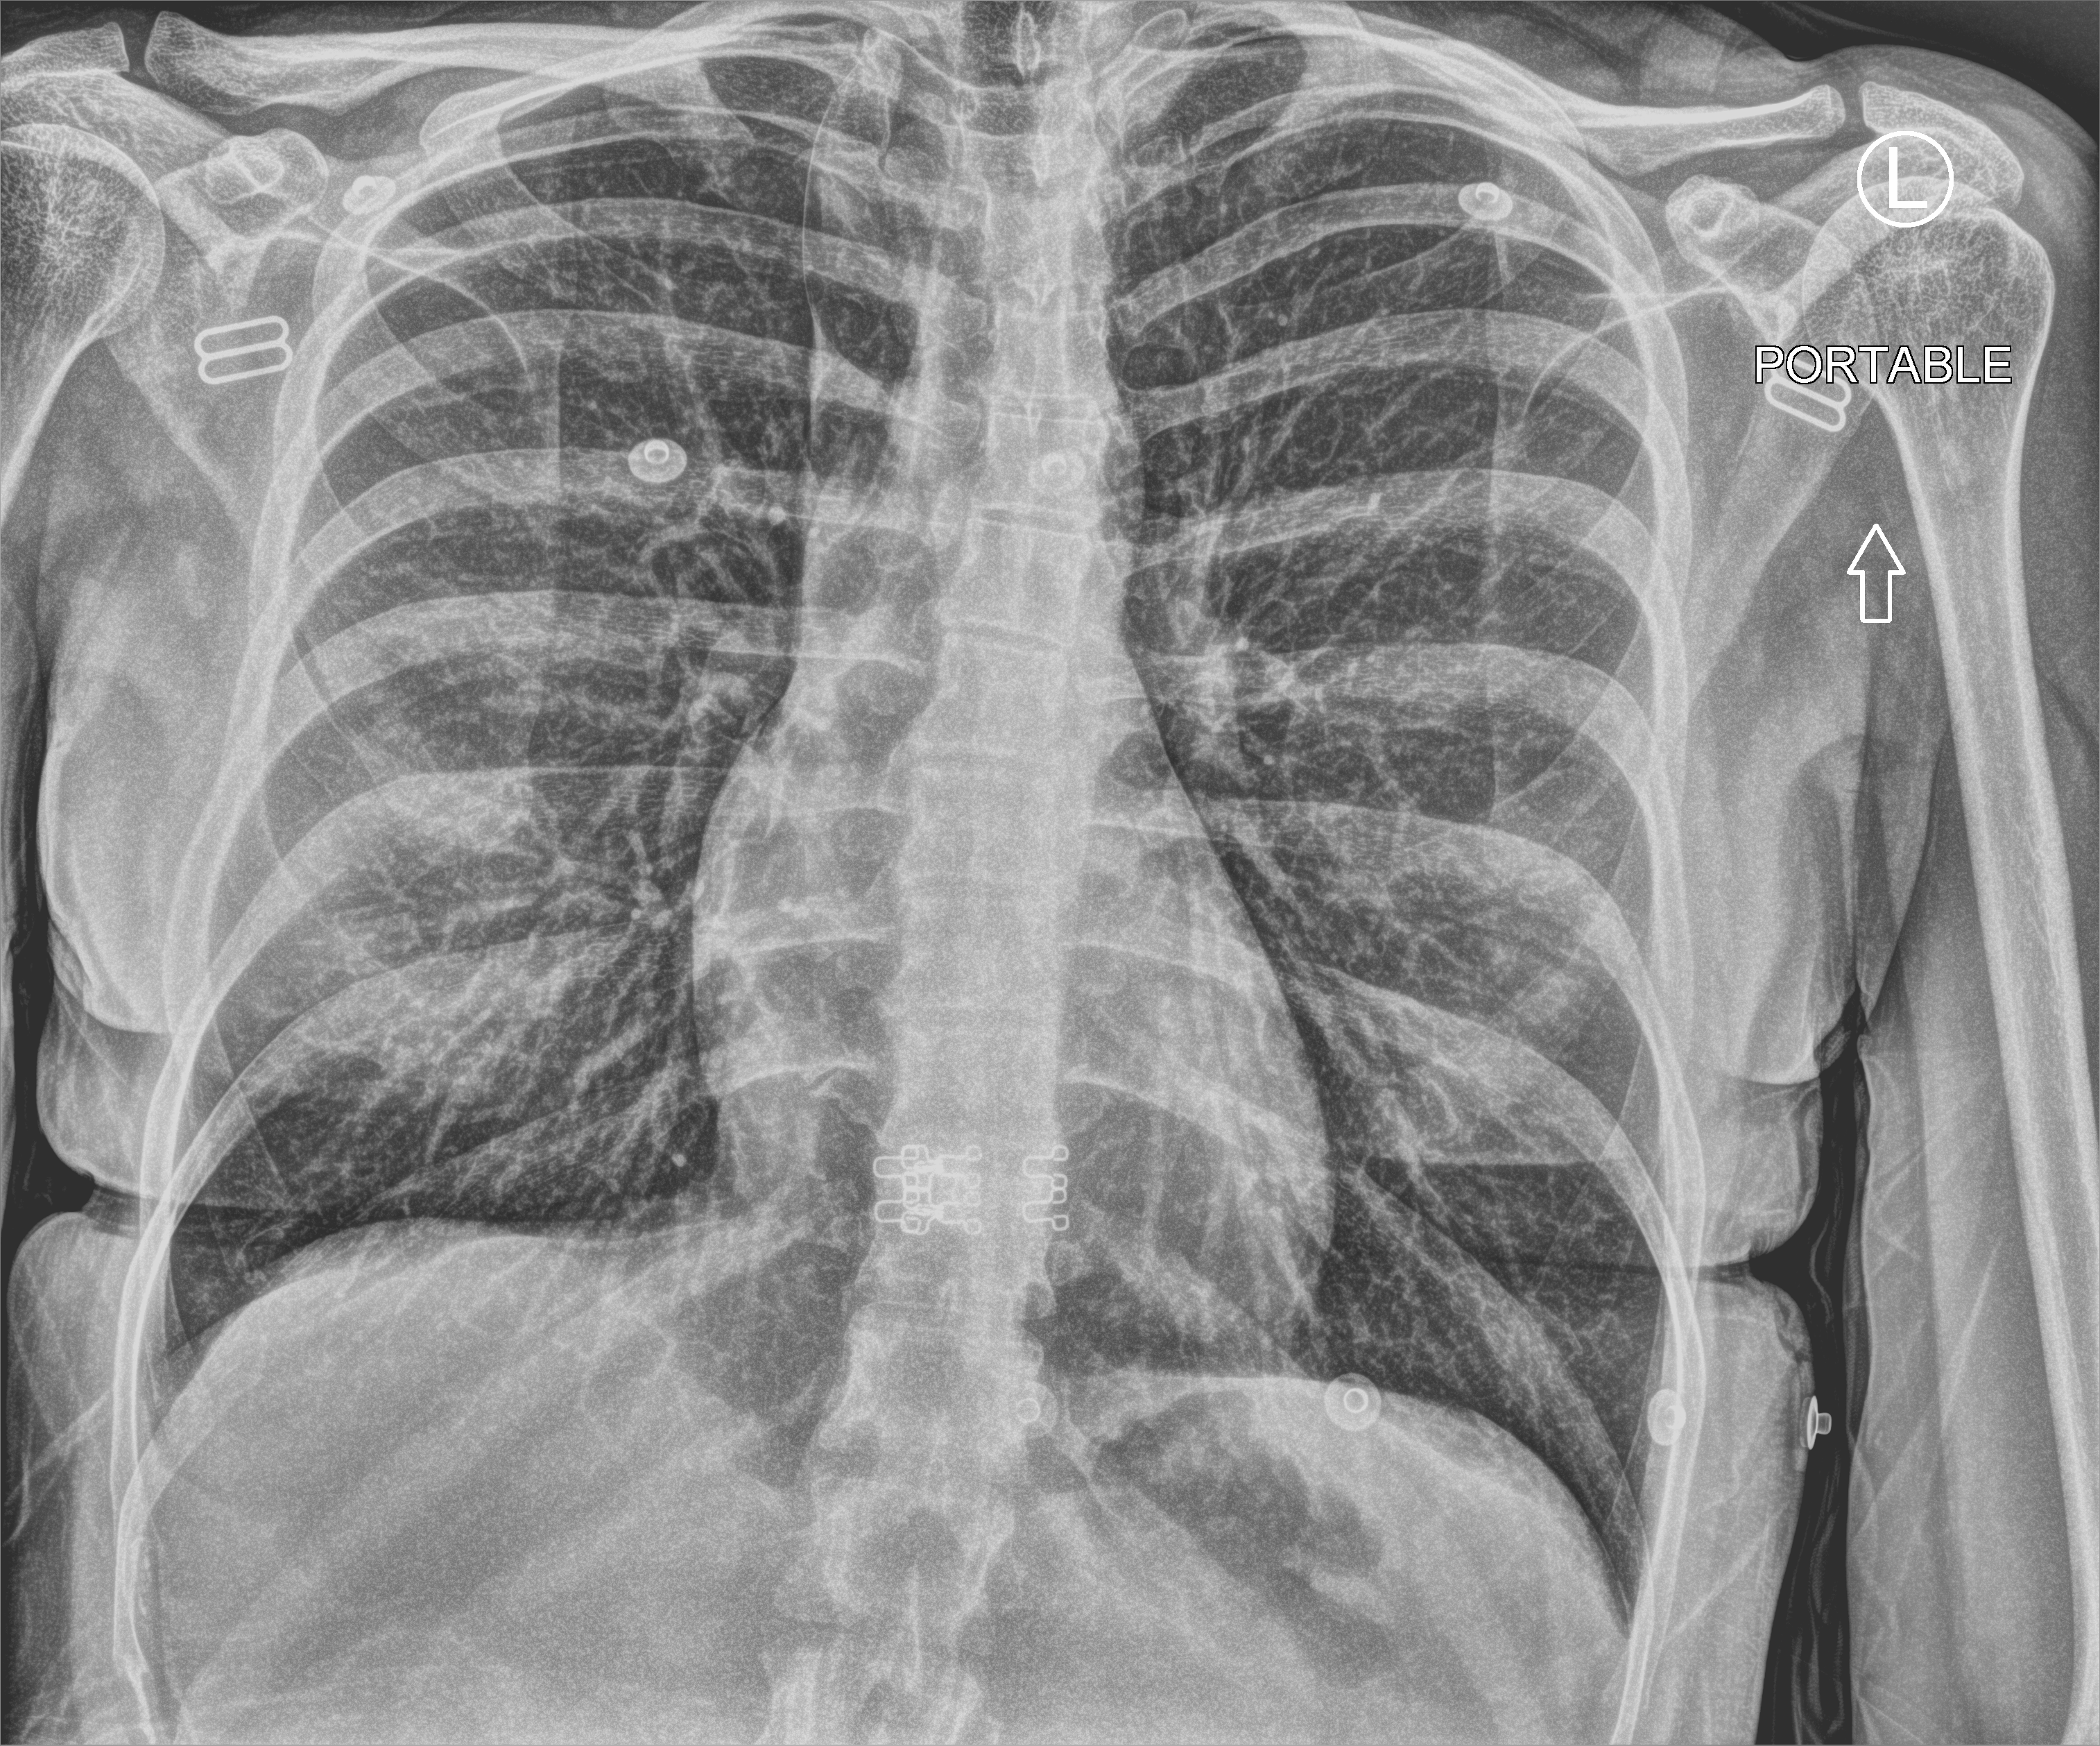
Bedside chest radiograph (computed radiography), anteroposterior (AP) projection. Patient hospitalised with COVID-19; female, aged 18–59 years.
Admission-level facts for this patient (not findings on this image; timing relative to this image not recorded): mechanically ventilated during this hospital stay: no.